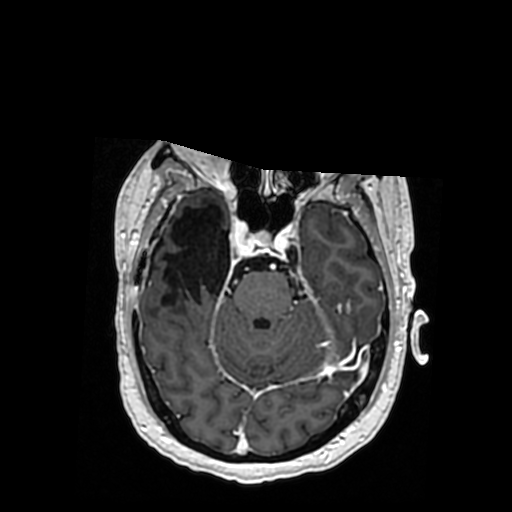
Brain MRI from a brain-tumour surgery series, one axial slice; slice 235 of 364 in the series (ordered by position); T1-weighted post-contrast; 512 × 512 image matrix, field of view 260 × 260 mm. Case-level facts recorded for this patient, not image findings: histopathology: Oligodendroglioma; WHO grade: 3; IDH mutation: yes; tumour location: Right Posterior Temporal Inferior Parietal.
Outlined on this slice (expert manual segmentation):
- previous resection cavity: box from (x=162, y=205) to (x=230, y=305) px